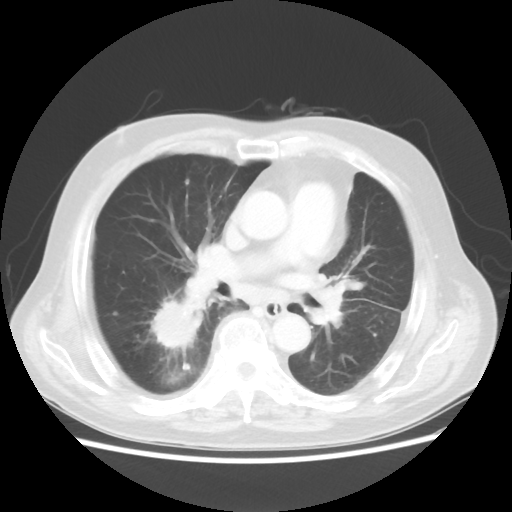
Chest CT, one axial slice; position 20 of 44 along the scan axis; 100 kVp; lung window (W 1500 / L -600 HU); 5 mm slice thickness; 512 × 512 image matrix, field of view 359 × 359 mm. Patient: male, 83 years. From the clinical record (not read from this slice): clinical TNM (as recorded): T2 N3 M0.
Annotated regions visible in this slice (bounding box drawn by a radiologist):
- lung tumour (recorded histology: adenocarcinoma): bounding box [x1, y1, x2, y2] px = [139, 289, 204, 352]